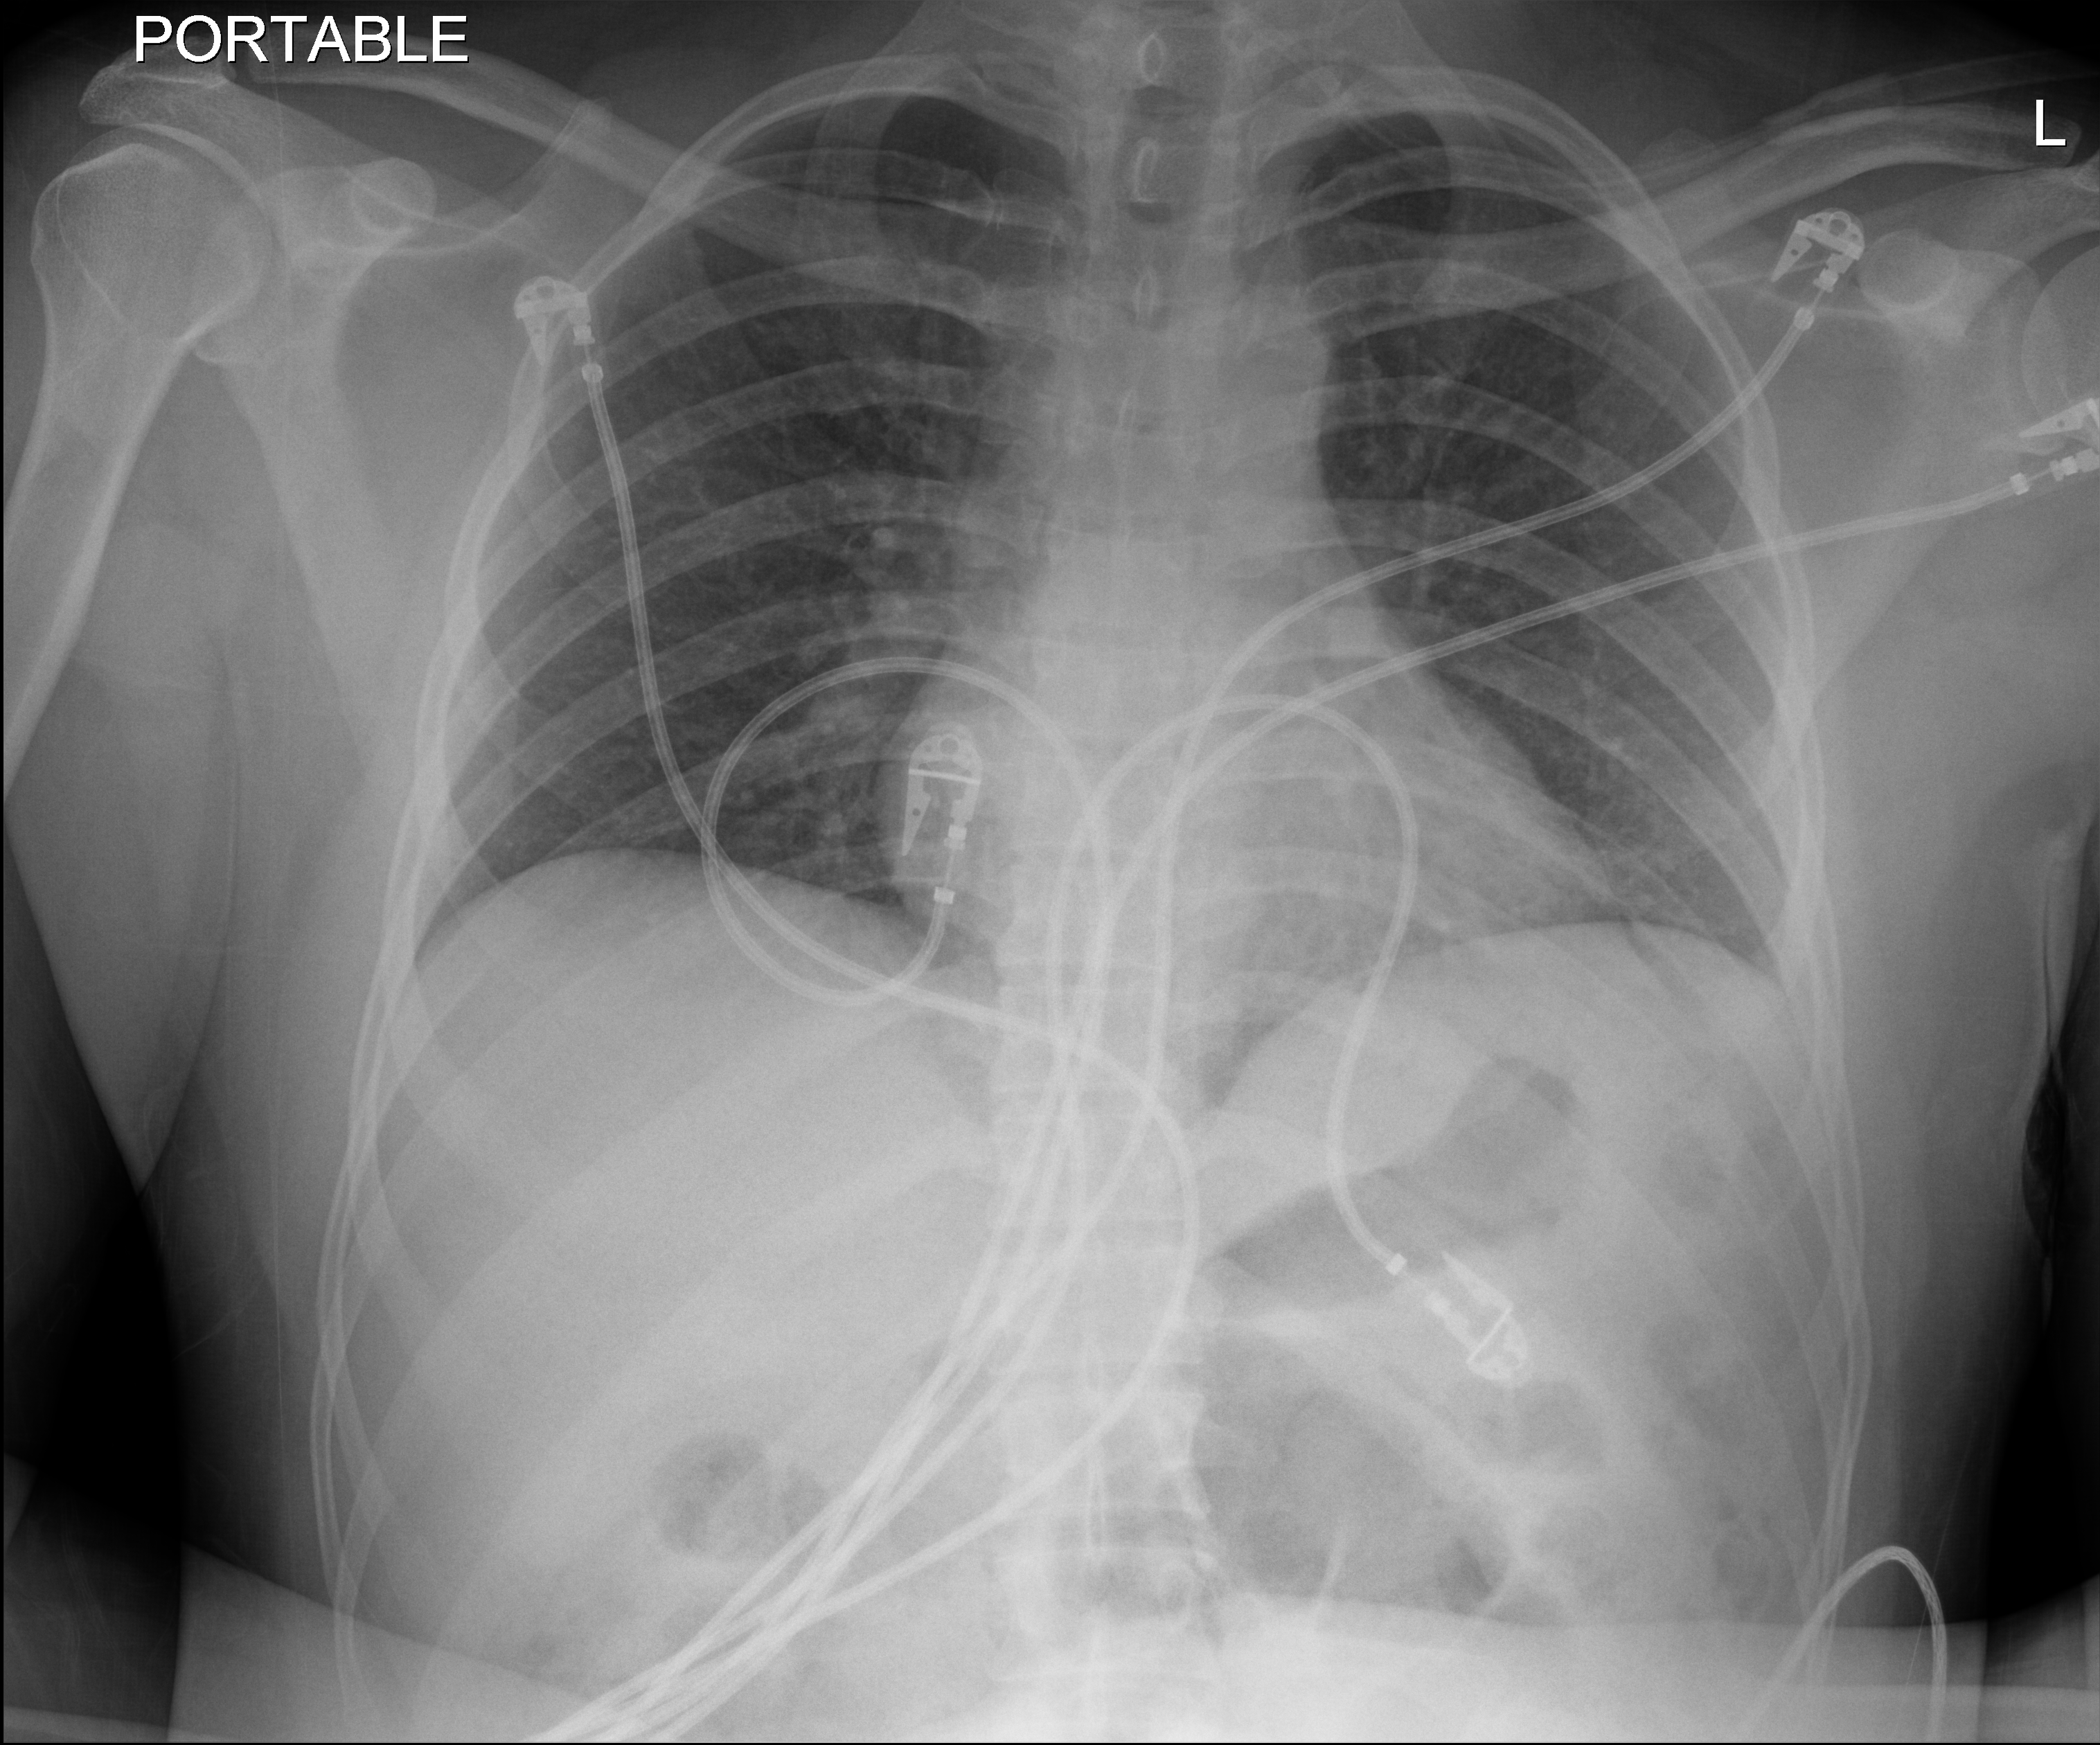
Bedside chest radiograph (digital radiography); anteroposterior (AP) projection. Male patient hospitalised with COVID-19, age 18–59 years.
From the hospital-stay record, not from the radiograph (when in the stay this image was taken is not recorded): mechanically ventilated during this hospital stay: no.